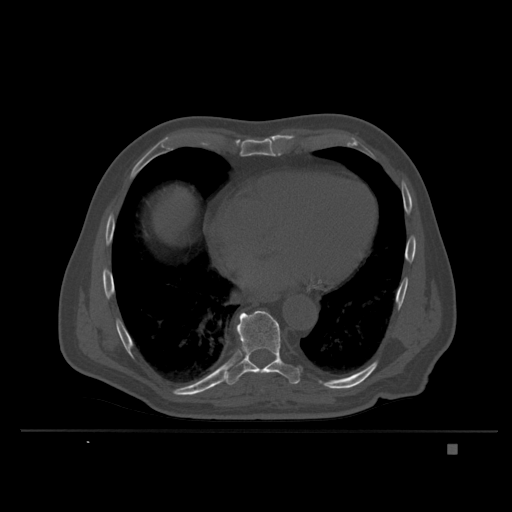
CT including the spine, one axial slice; slice 215 of 435 in the series (ordered by position); bone window (W 1800 / L 400 HU); 1.5 mm slice thickness; 512 × 512 image matrix, field of view 434 × 434 mm. Male patient, age 73 years. Case-level facts recorded for this patient, not image findings: primary cancer: skin.
Structures marked on this image (semi-automatically segmented with operator editing):
- T9 vertebra: bounding box [x1, y1, x2, y2] px = [225, 311, 301, 385]